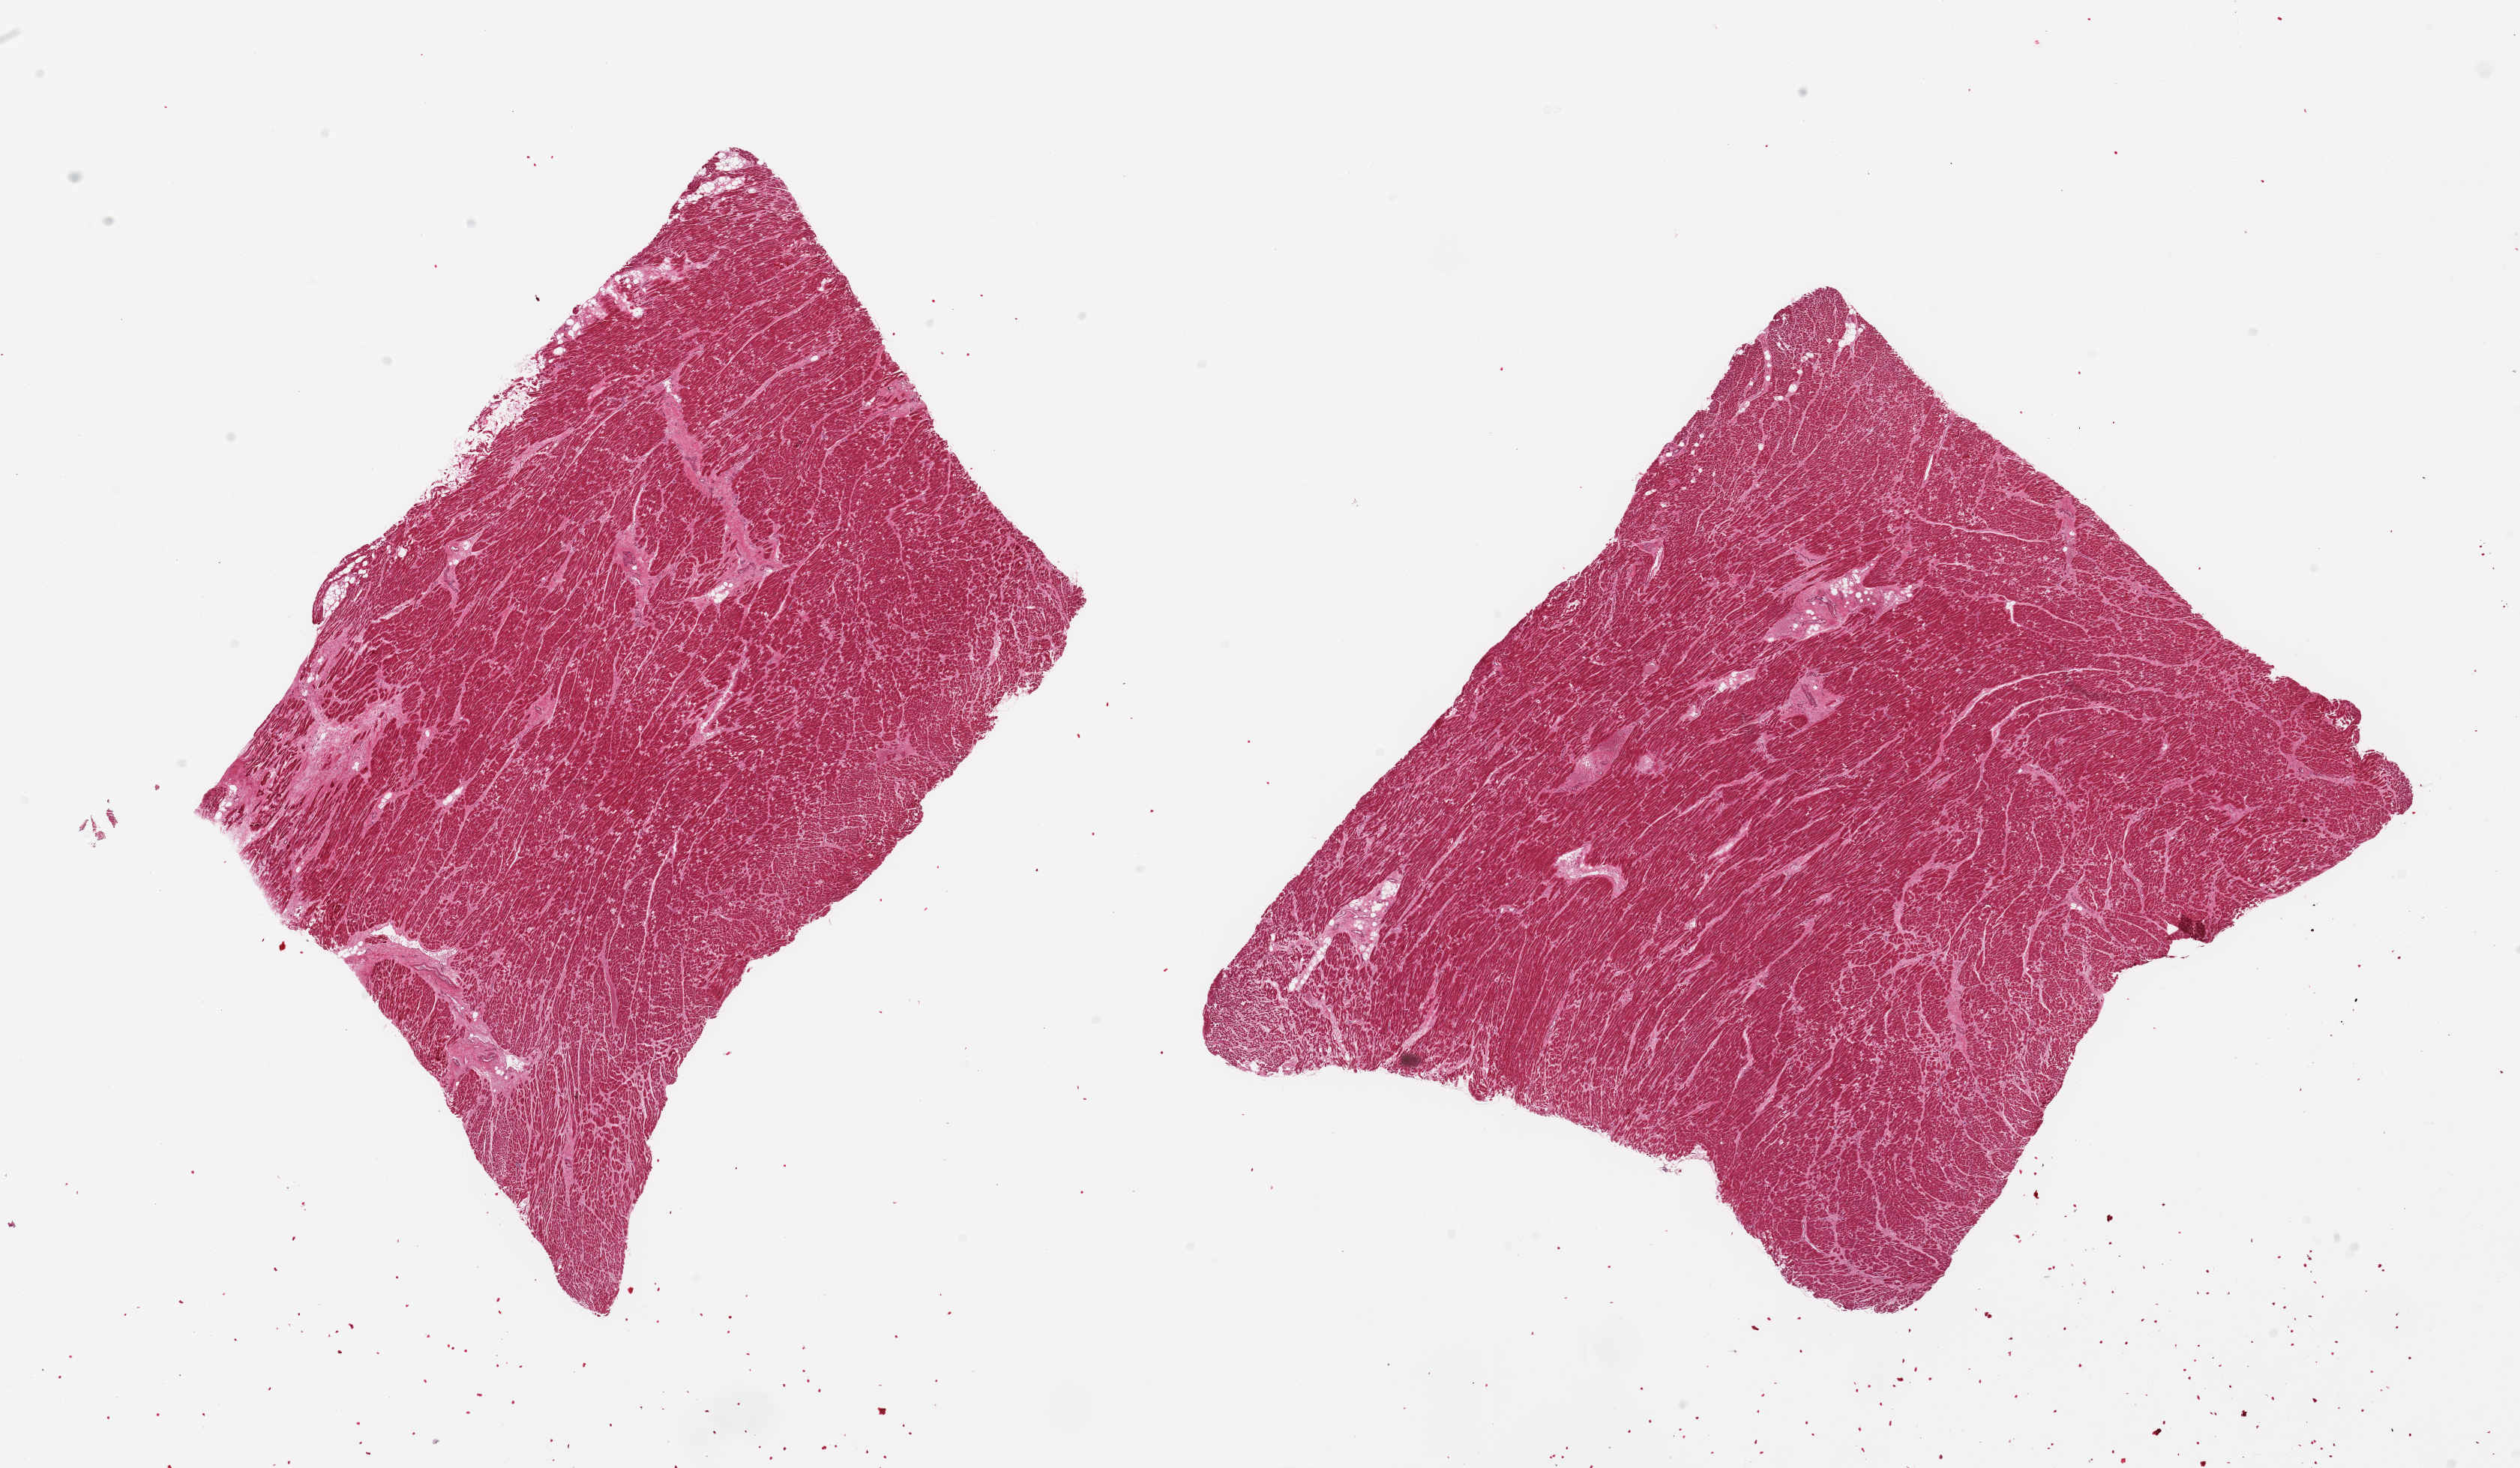
Hematoxylin and eosin (H&E) whole-slide image, brightfield, whole scanned area (about 26.6 x 15.5 mm) shown as a low-resolution overview; PAXgene-fixed paraffin-embedded (PFPE) section; section of heart (target tissue); donor tissue sample. Male donor.
Reviewer comment on this tissue sample: 2 pieces, marked chronic ischemic changes/interstitial fibrosis, remote micro-infarcts present.